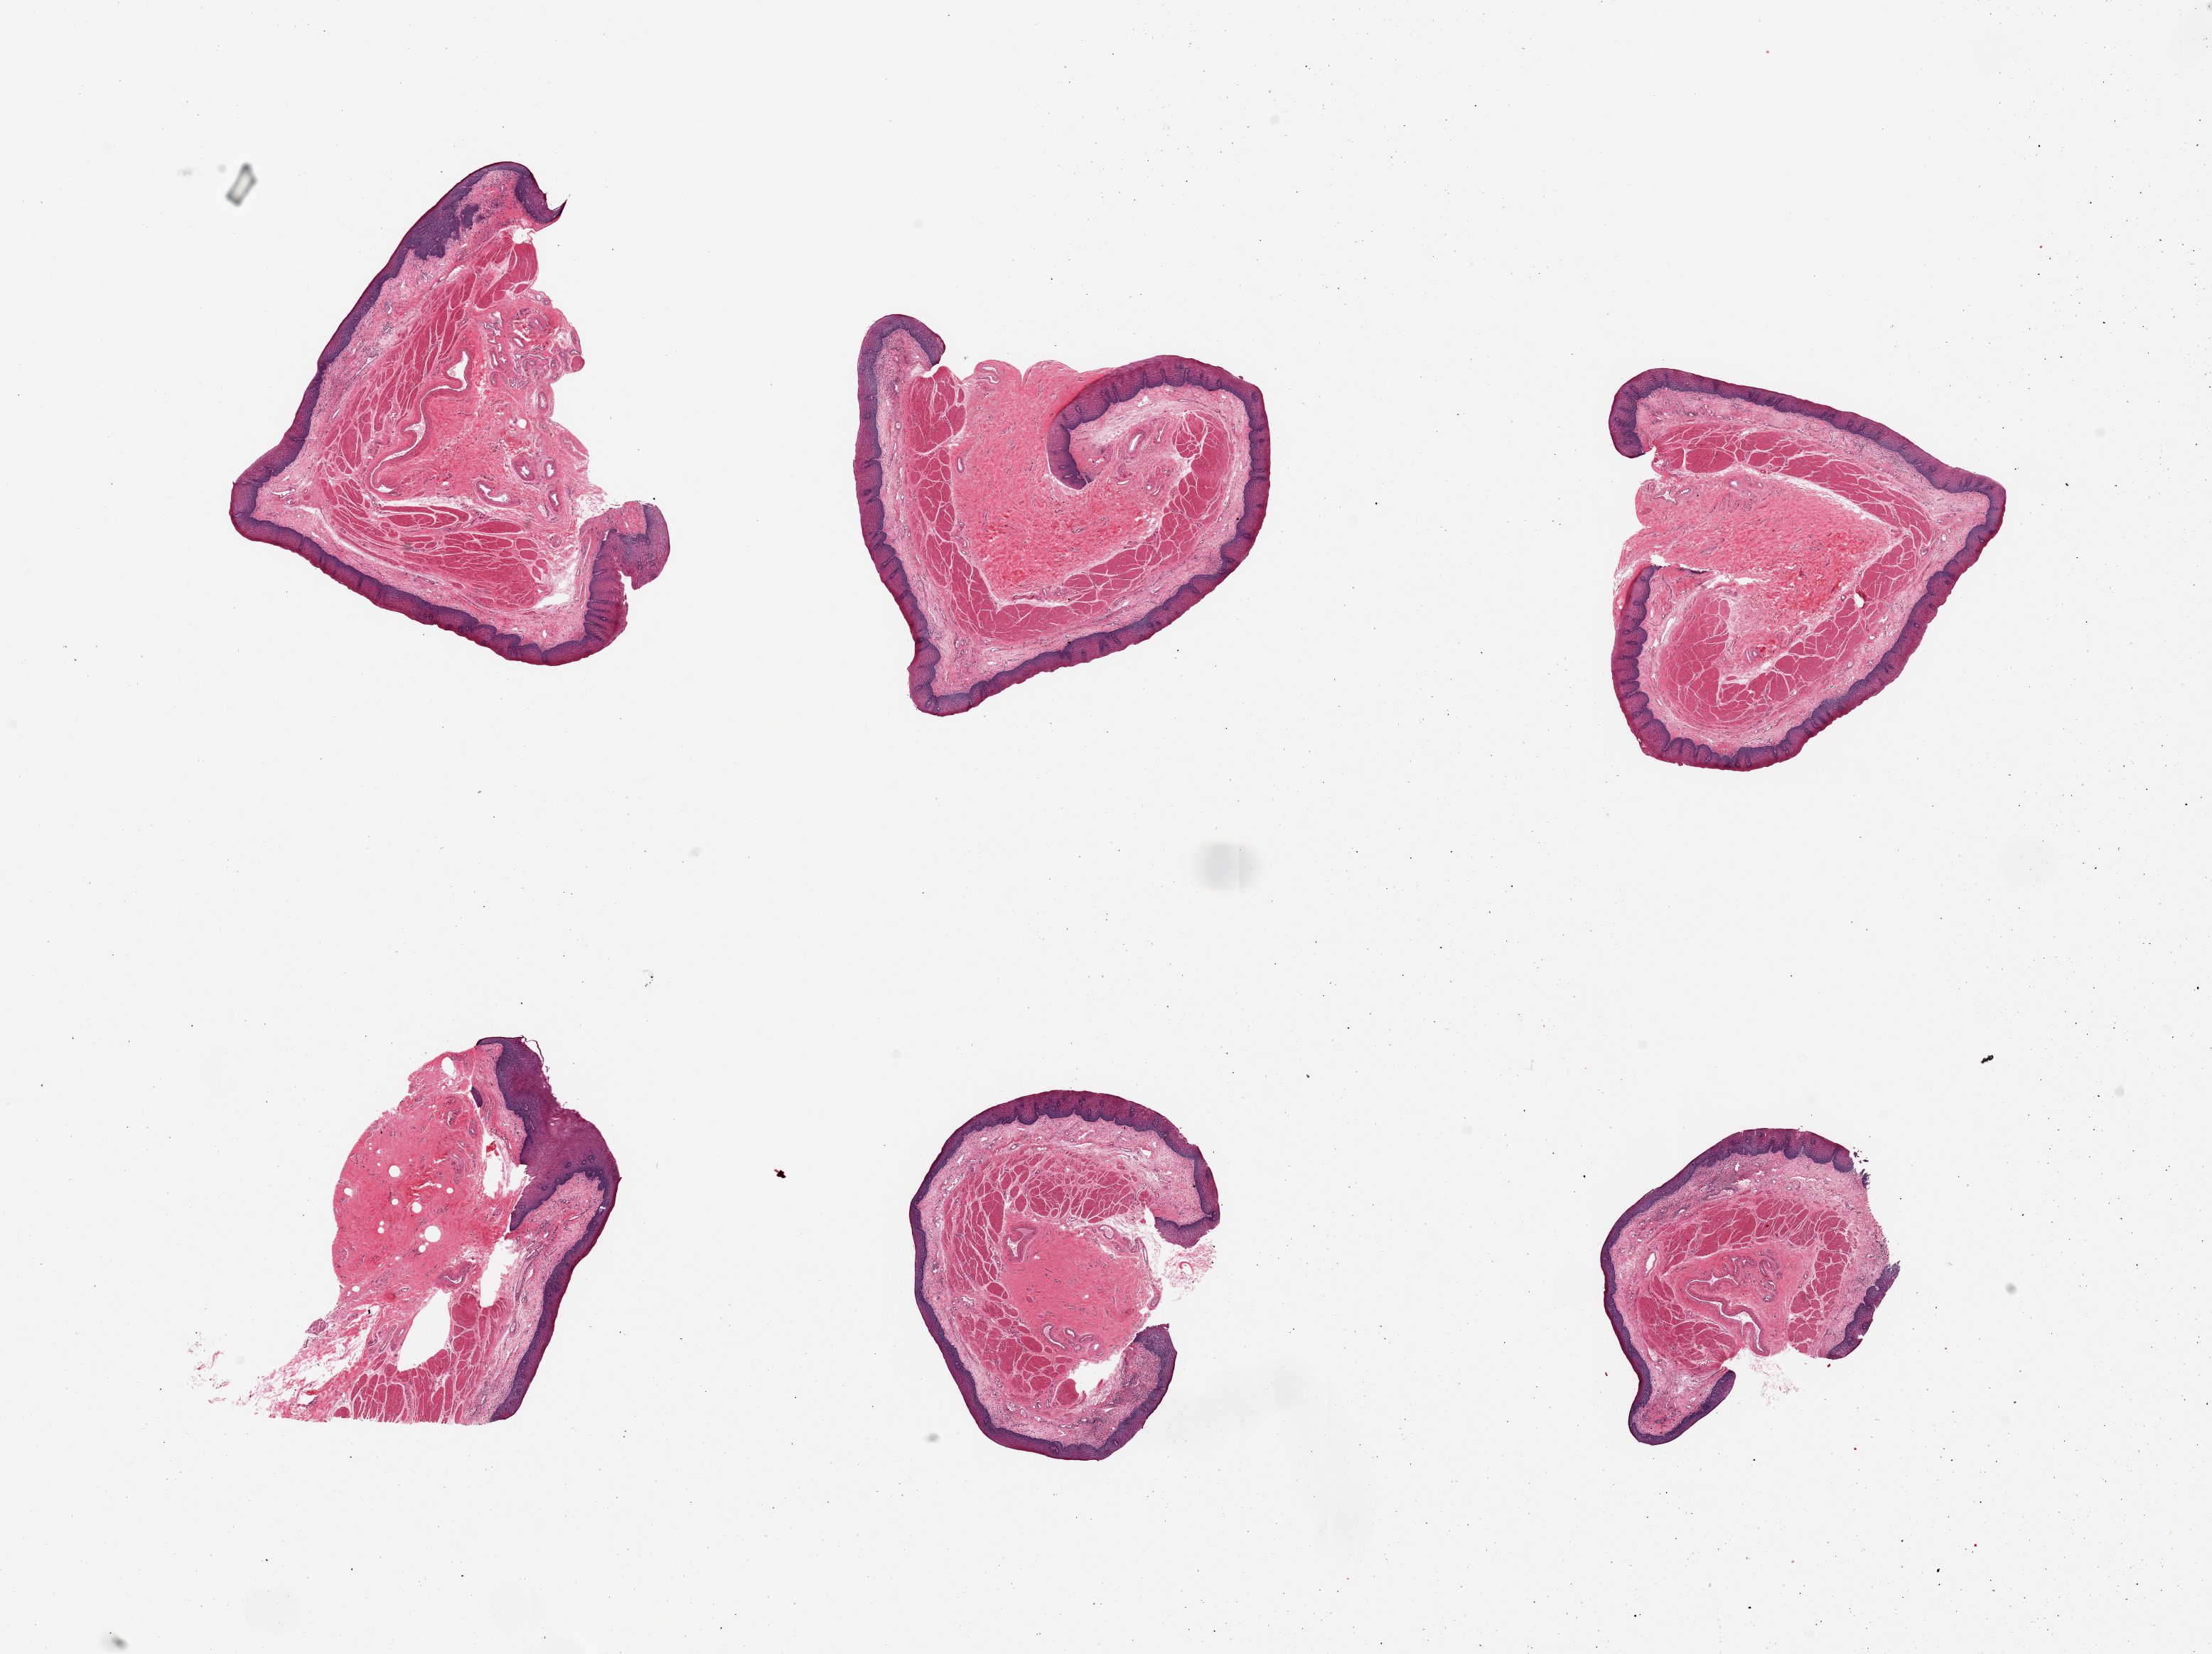
Digitized H&E-stained section — low-resolution overview of the scanned area, about 24.6 x 18.4 mm (from a 20x scan), PAXgene-fixed paraffin-embedded (PFPE) section, section of esophageal mucous membrane (target tissue), tissue donor sample. Donor sex: female.
• reviewer comment on this tissue sample: 6 pieces, squamous mucosa up to ~0.3mm, ~10% thickness